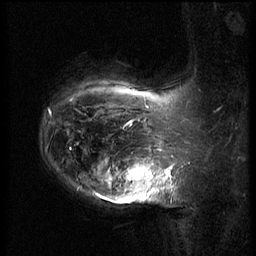
Breast MRI (dynamic contrast-enhanced), one sagittal slice; position 50 of 62 along the scan axis; 3 images stored at this slice position (order not interpretable as contrast timing); 1.5 T; TE 4.2 ms, TR 8.9 ms; 2.5 mm slice thickness; 256 × 256 image matrix, field of view 200 × 200 mm. Patient: female, 37 years. From the clinical record (not read from this slice): setting: breast cancer imaged before/during neoadjuvant chemotherapy; receptor status: triple-negative.
Outlined on this slice (semi-automatically segmented with operator editing):
- analysis volume of interest (the breast-tissue region the enhancement analysis was run in; not a lesion): box from (x=116, y=146) to (x=168, y=203) px
- tumour enhancement mask (voxels above the 140 % enhancement threshold inside the analysis volume of interest): (x=123, y=166)–(x=168, y=202)